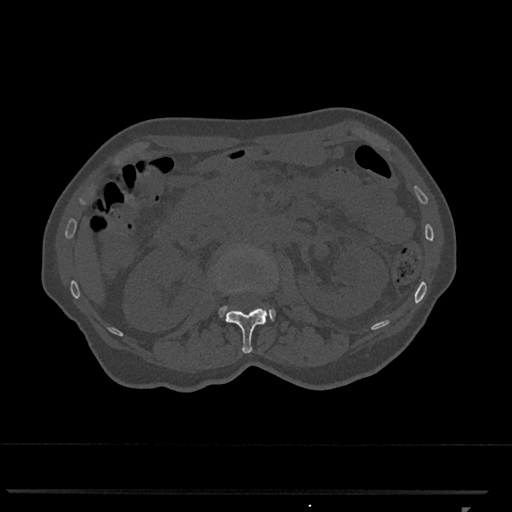
CT including the spine, one axial slice. Reconstruction kernel Br40s/3. 120 kVp. Bone window (W 1800 / L 400 HU). 0.5 mm slice thickness. 512 × 512 image matrix, field of view 380 × 380 mm. Female patient, age 62 years. Case-level facts recorded for this patient, not image findings: primary cancer: renal.
Annotated regions visible in this slice (semi-automatically segmented with operator editing):
- L1 vertebra: box from (x=225, y=285) to (x=267, y=354) px
- L2 vertebra: (x=218, y=253)–(x=276, y=321)